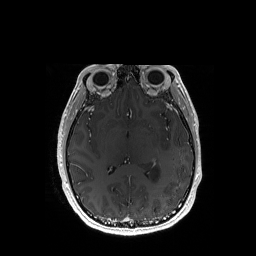
Brain MRI from a brain-tumour surgery series, one axial slice. Position 90 of 192 along the scan axis. T1-weighted post-contrast. 1 mm slice thickness. 256 × 256 image matrix, field of view 256 × 256 mm. Case-level facts recorded for this patient, not image findings: histopathology: Astrocytoma; WHO grade: 3; IDH mutation: yes.
Structures marked on this image (outlined manually by an expert reader):
- tumour: bounding box <151,164,160,182> (left, top, right, bottom; pixels)